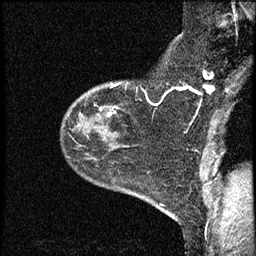
Breast MRI (dynamic contrast-enhanced), one sagittal slice; slice 49 of 60 in the series (ordered by position); dynamic contrast-enhanced study with each time point stored as its own series, time point 2 of 4 at this slice position (early post-contrast, ordered by acquisition time); 1.5 T; TE 4.2 ms, TR 17.6 ms; 2 mm slice thickness; 256 × 256 image matrix. Patient: female, 53 years. Case-level facts recorded for this patient, not image findings: setting: breast cancer imaged before/during neoadjuvant chemotherapy; receptor status: HR-positive, HER2-negative.
Structures marked on this image (semi-automatic segmentation, software-assisted and operator-edited):
- analysis volume of interest (the breast-tissue region the enhancement analysis was run in; not a lesion): bounding box [x1, y1, x2, y2] px = [61, 82, 154, 199]
- tumour enhancement mask (voxels above the 100 % enhancement threshold inside the analysis volume of interest): [107, 107, 118, 116]